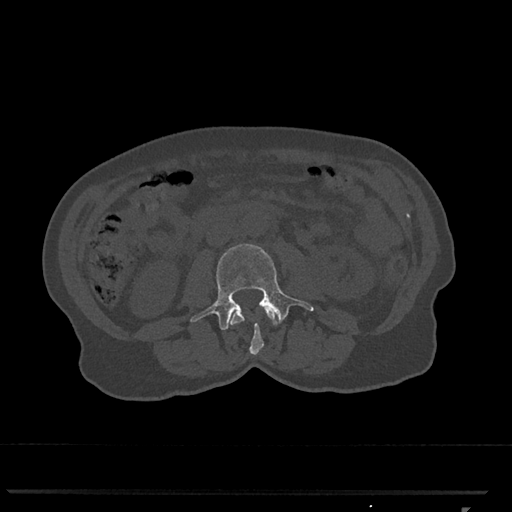
CT including the spine, one axial slice. Position 290 of 793 along the scan axis. Reconstruction kernel Br40s/3. 120 kVp. Bone window (W 1800 / L 400 HU). 0.5 mm slice thickness. 512 × 512 image matrix, field of view 380 × 380 mm. Female patient, age 62 years. From the clinical record (not read from this slice): primary cancer: renal.
Annotated regions visible in this slice (semi-automatic segmentation, software-assisted and operator-edited):
- L2 vertebra: bounding box <229,307,278,355> (left, top, right, bottom; pixels)
- L3 vertebra: <190,244,314,330>